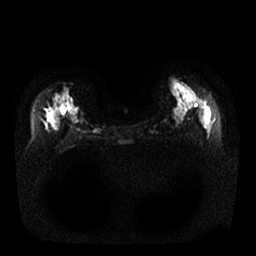
Breast MRI, one axial slice. Slice 14 of 25 in the series (ordered by position). Diffusion-weighted series; image 2 of 4 stored at this slice position (different b-values; order by instance number). 1.5 T. 256 × 256 image matrix. Female patient.
Annotated regions visible in this slice (outlined manually by an expert reader):
- tumour on diffusion-weighted imaging: box from (x=51, y=109) to (x=55, y=117) px